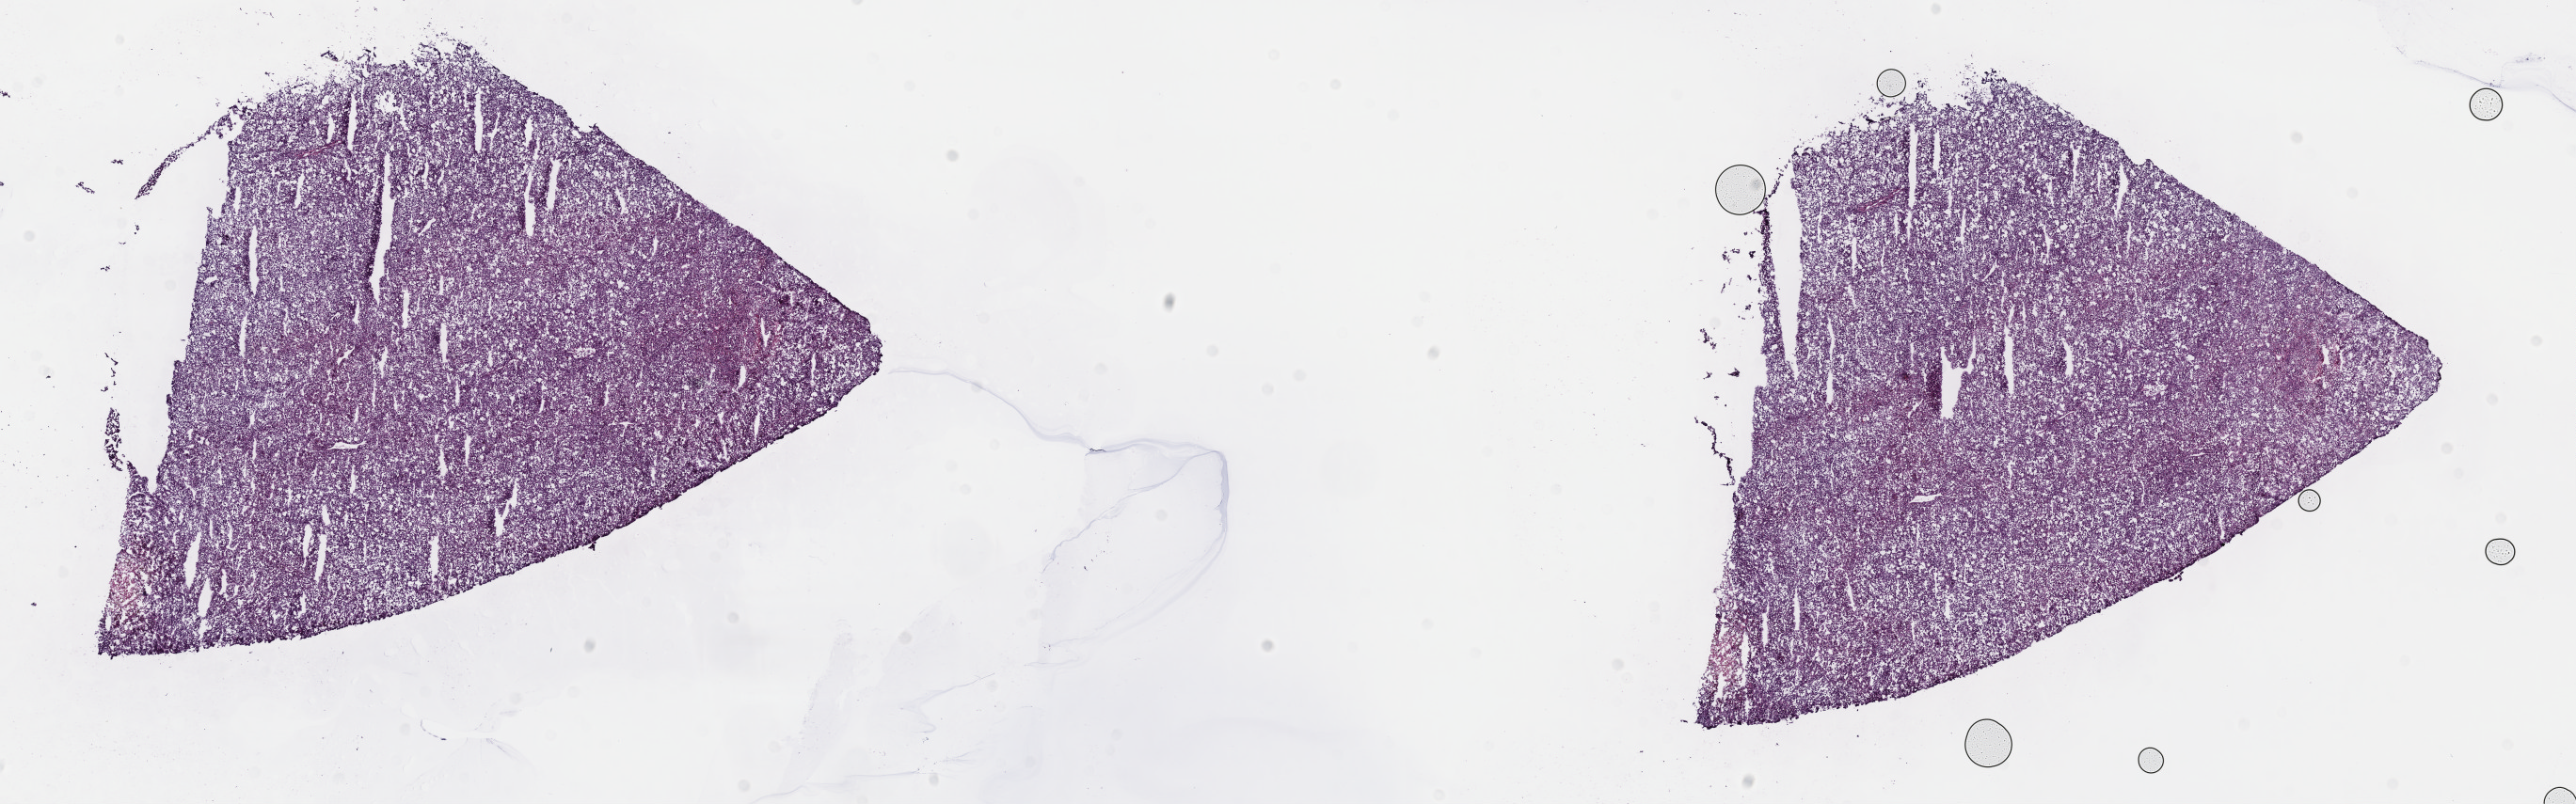
Whole-slide histology image, H&E-stained — shown as a low-resolution overview of the whole scanned area (about 22.1 x 6.9 mm, acquisition: 40x scan). Frozen section from the top of the tissue portion. Sample: primary tumour, liver. Male, age 70 years at initial diagnosis. Histologic grade: G2 (moderately differentiated). Composition of this section per pathologist review: tumour cells 80%, tumour nuclei 80%, normal cells 0%, stromal cells 20%, necrosis 0%. Infiltration values recorded for this section: lymphocyte infiltration 3%, monocyte infiltration 1%, neutrophil infiltration 1%.
Histologic diagnosis: Hepatocellular carcinoma, NOS. AJCC pathologic stage: I.